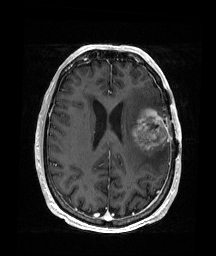
Brain MRI from a brain-tumour surgery series, one axial slice; position 72 of 176 along the scan axis; T1-weighted post-contrast; 1 mm slice thickness; 216 × 256 image matrix, field of view 219 × 260 mm. From the clinical record (not read from this slice): histopathology: Glioblastoma; WHO grade: 4; IDH mutation: no; tumour location: Left Frontal.
Annotated regions visible in this slice (outlined manually by an expert reader):
- tumour: bounding box (x1, y1, x2, y2) in pixels: (132, 108, 168, 154)